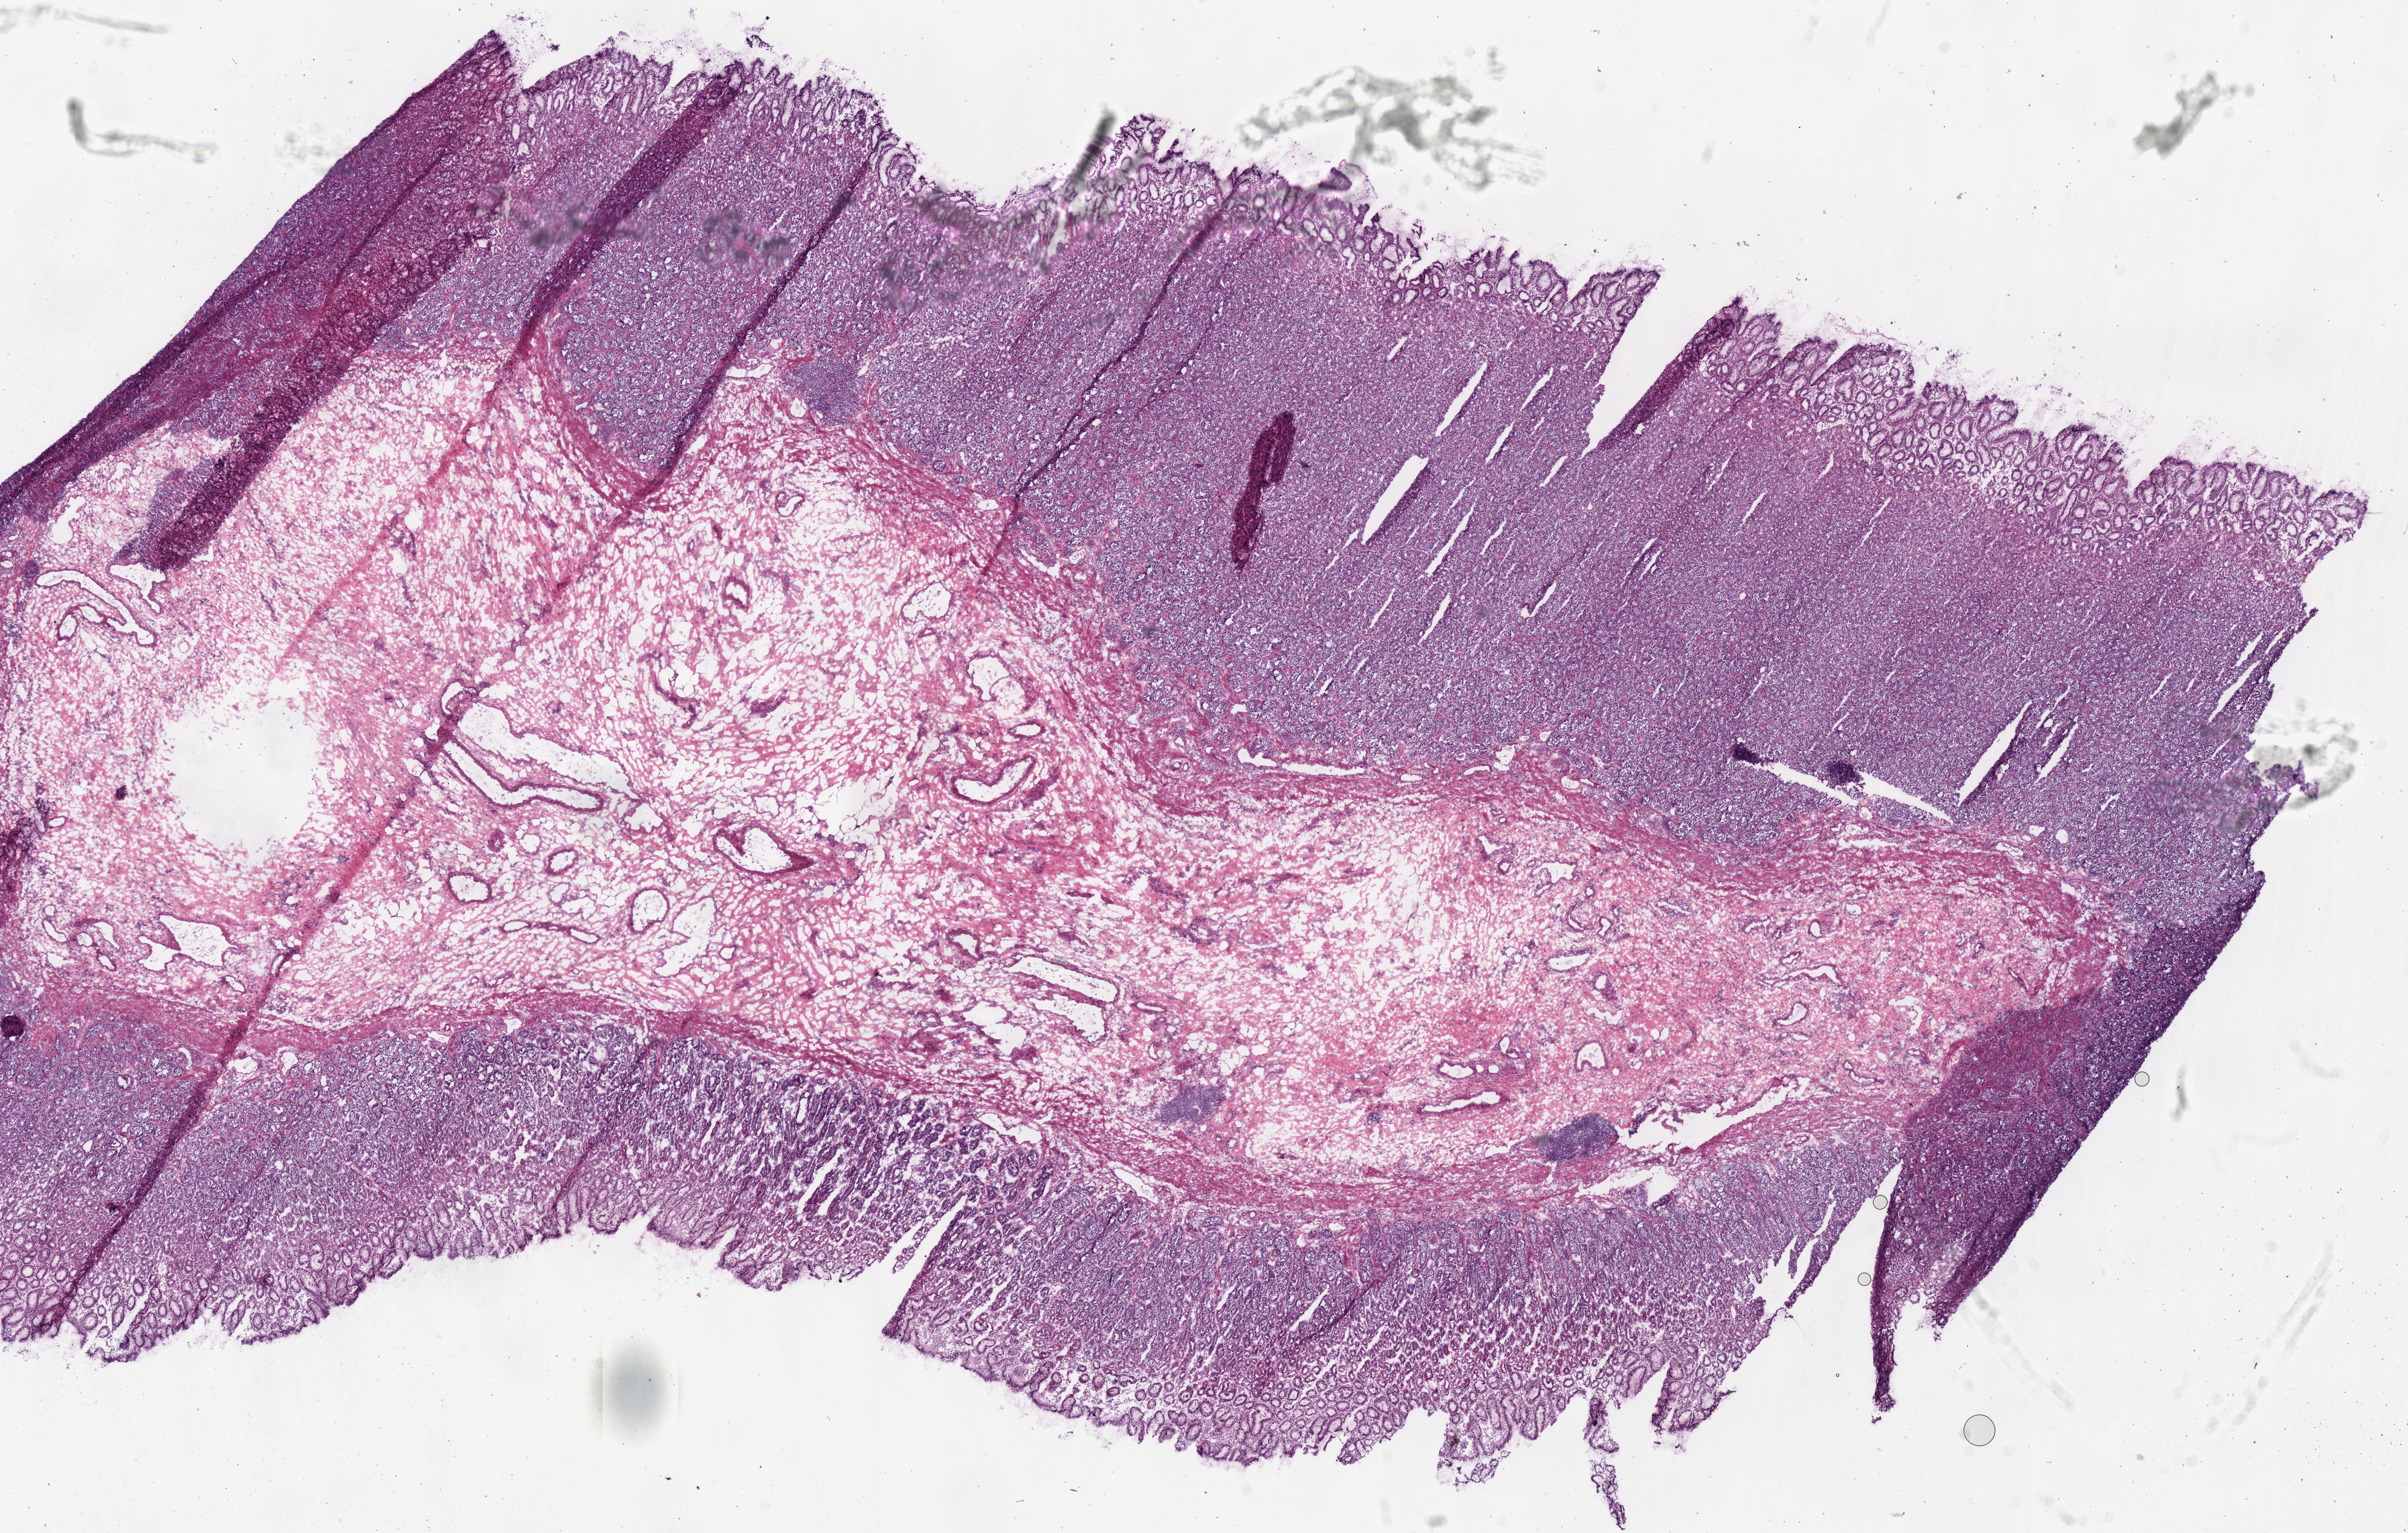
H&E whole-slide image — a low-resolution overview of the entire scanned area, about 15.7 x 10.0 mm (slide scanned at 40x). Frozen section from the bottom of the tissue portion. Sample: solid tissue normal (non-tumour tissue), stomach. Male, age 41 years at initial diagnosis.
This section: solid tissue normal sample (biorepository sample class). Patient diagnosis: Adenocarcinoma, NOS (cardia, NOS).